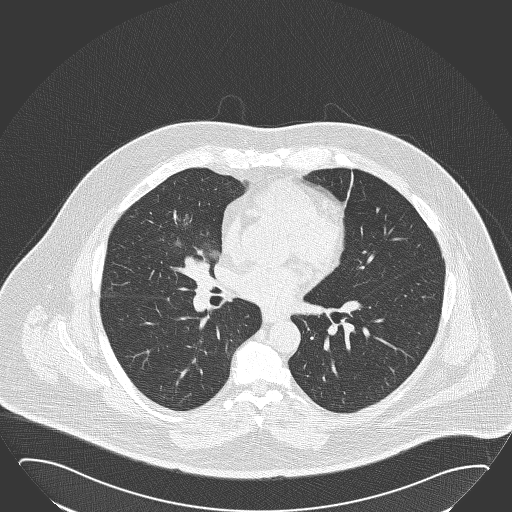
Chest CT (low-dose screening protocol), one axial image, first (baseline) screen, lung window (W 1500 / L -600 HU), 2 mm slice thickness, lung (sharp) reconstruction kernel (B50f), slice 88 of 168 in the series. Male participant, aged 61 years at enrolment. Former smoker at enrolment.
Expert reader's lesion annotation, box from (x=148, y=207) to (x=232, y=293) px. The screening reader recorded 2 non-calcified nodules or masses ≥4 mm on this exam (right middle lobe, left lower lobe); which of them this box marks is not recorded. Official screen result: positive, change unspecified: nodule(s) >= 4 mm or enlarging nodule(s), mass(es), or other non-specific abnormalities suspicious for lung cancer. Participant outcome: lung cancer diagnosed 47 days after this screen — basaloid squamous cell carcinoma, right middle lobe, right hilum, poorly differentiated (G3), stage IIB (AJCC 6th edition), 95 mm at pathology.